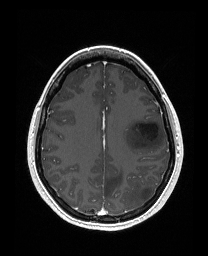
Brain MRI from a brain-tumour surgery series, one axial slice; position 110 of 176 along the scan axis; T1-weighted post-contrast; 1 mm slice thickness; 208 × 256 image matrix, field of view 203 × 250 mm. Case-level facts recorded for this patient, not image findings: histopathology: Astrocytoma; WHO grade: 3; IDH mutation: yes.
Outlined on this slice (manually delineated by an expert):
- tumour: bounding box [x1, y1, x2, y2] px = [122, 119, 165, 154]